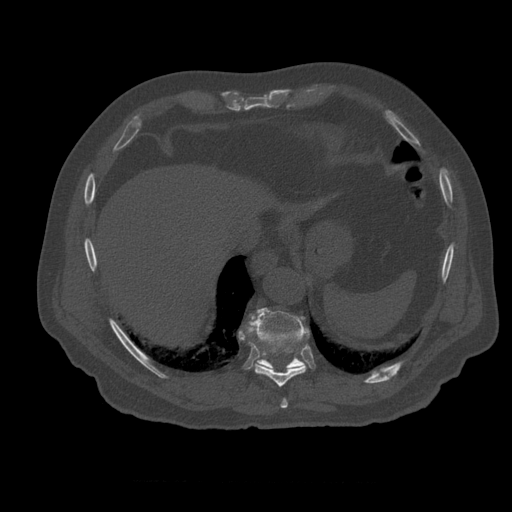
CT including the spine, one axial slice; reconstruction kernel STANDARD; bone window (W 1800 / L 400 HU); 512 × 512 image matrix, field of view 407 × 407 mm. Patient age 73 years. From the clinical record (not read from this slice): primary cancer: prostate.
Structures marked on this image (semi-automatic segmentation, software-assisted and operator-edited):
- T10 vertebra: box from (x=243, y=308) to (x=310, y=370) px
- T12 vertebra: (x=268, y=348)–(x=279, y=358)
- T8 vertebra: (x=281, y=399)–(x=288, y=409)
- T9 vertebra: (x=239, y=336)–(x=307, y=387)